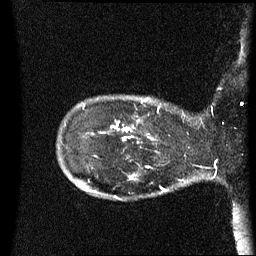
Breast MRI (dynamic contrast-enhanced), one sagittal slice. Position 12 of 60 along the scan axis. Dynamic contrast-enhanced series, image 2 of 3 at this slice position (ordered by acquisition). 1.5 T. TE 4.2 ms, TR 8.4 ms. 256 × 256 image matrix, field of view 220 × 220 mm. Female patient, age 41 years. From the clinical record (not read from this slice): setting: breast cancer imaged before/during neoadjuvant chemotherapy; receptor status: HER2-positive.
Outlined on this slice (semi-automatic segmentation, software-assisted and operator-edited):
- analysis volume of interest (the breast-tissue region the enhancement analysis was run in; not a lesion): bounding box (x1, y1, x2, y2) in pixels: (122, 96, 195, 137)
- tumour enhancement mask (voxels above the 70 % enhancement threshold inside the analysis volume of interest): (124, 108, 159, 137)